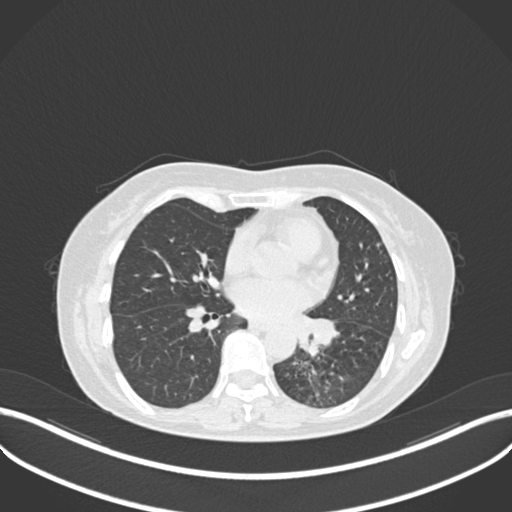
Chest CT, one axial slice. Position 121 of 270 along the scan axis. Reconstruction kernel B30f. Lung window (W 1500 / L -600 HU). 1 mm slice thickness. 512 × 512 image matrix. Patient: female, 63 years. Case-level facts recorded for this patient, not image findings: clinical TNM (as recorded): T1b N0 M0; histopathological grade: G2-3.
Structures marked on this image (rectangle marked by the reading radiologist):
- lung tumour (recorded histology: adenocarcinoma): bounding box (x1, y1, x2, y2) in pixels: (288, 311, 345, 361)